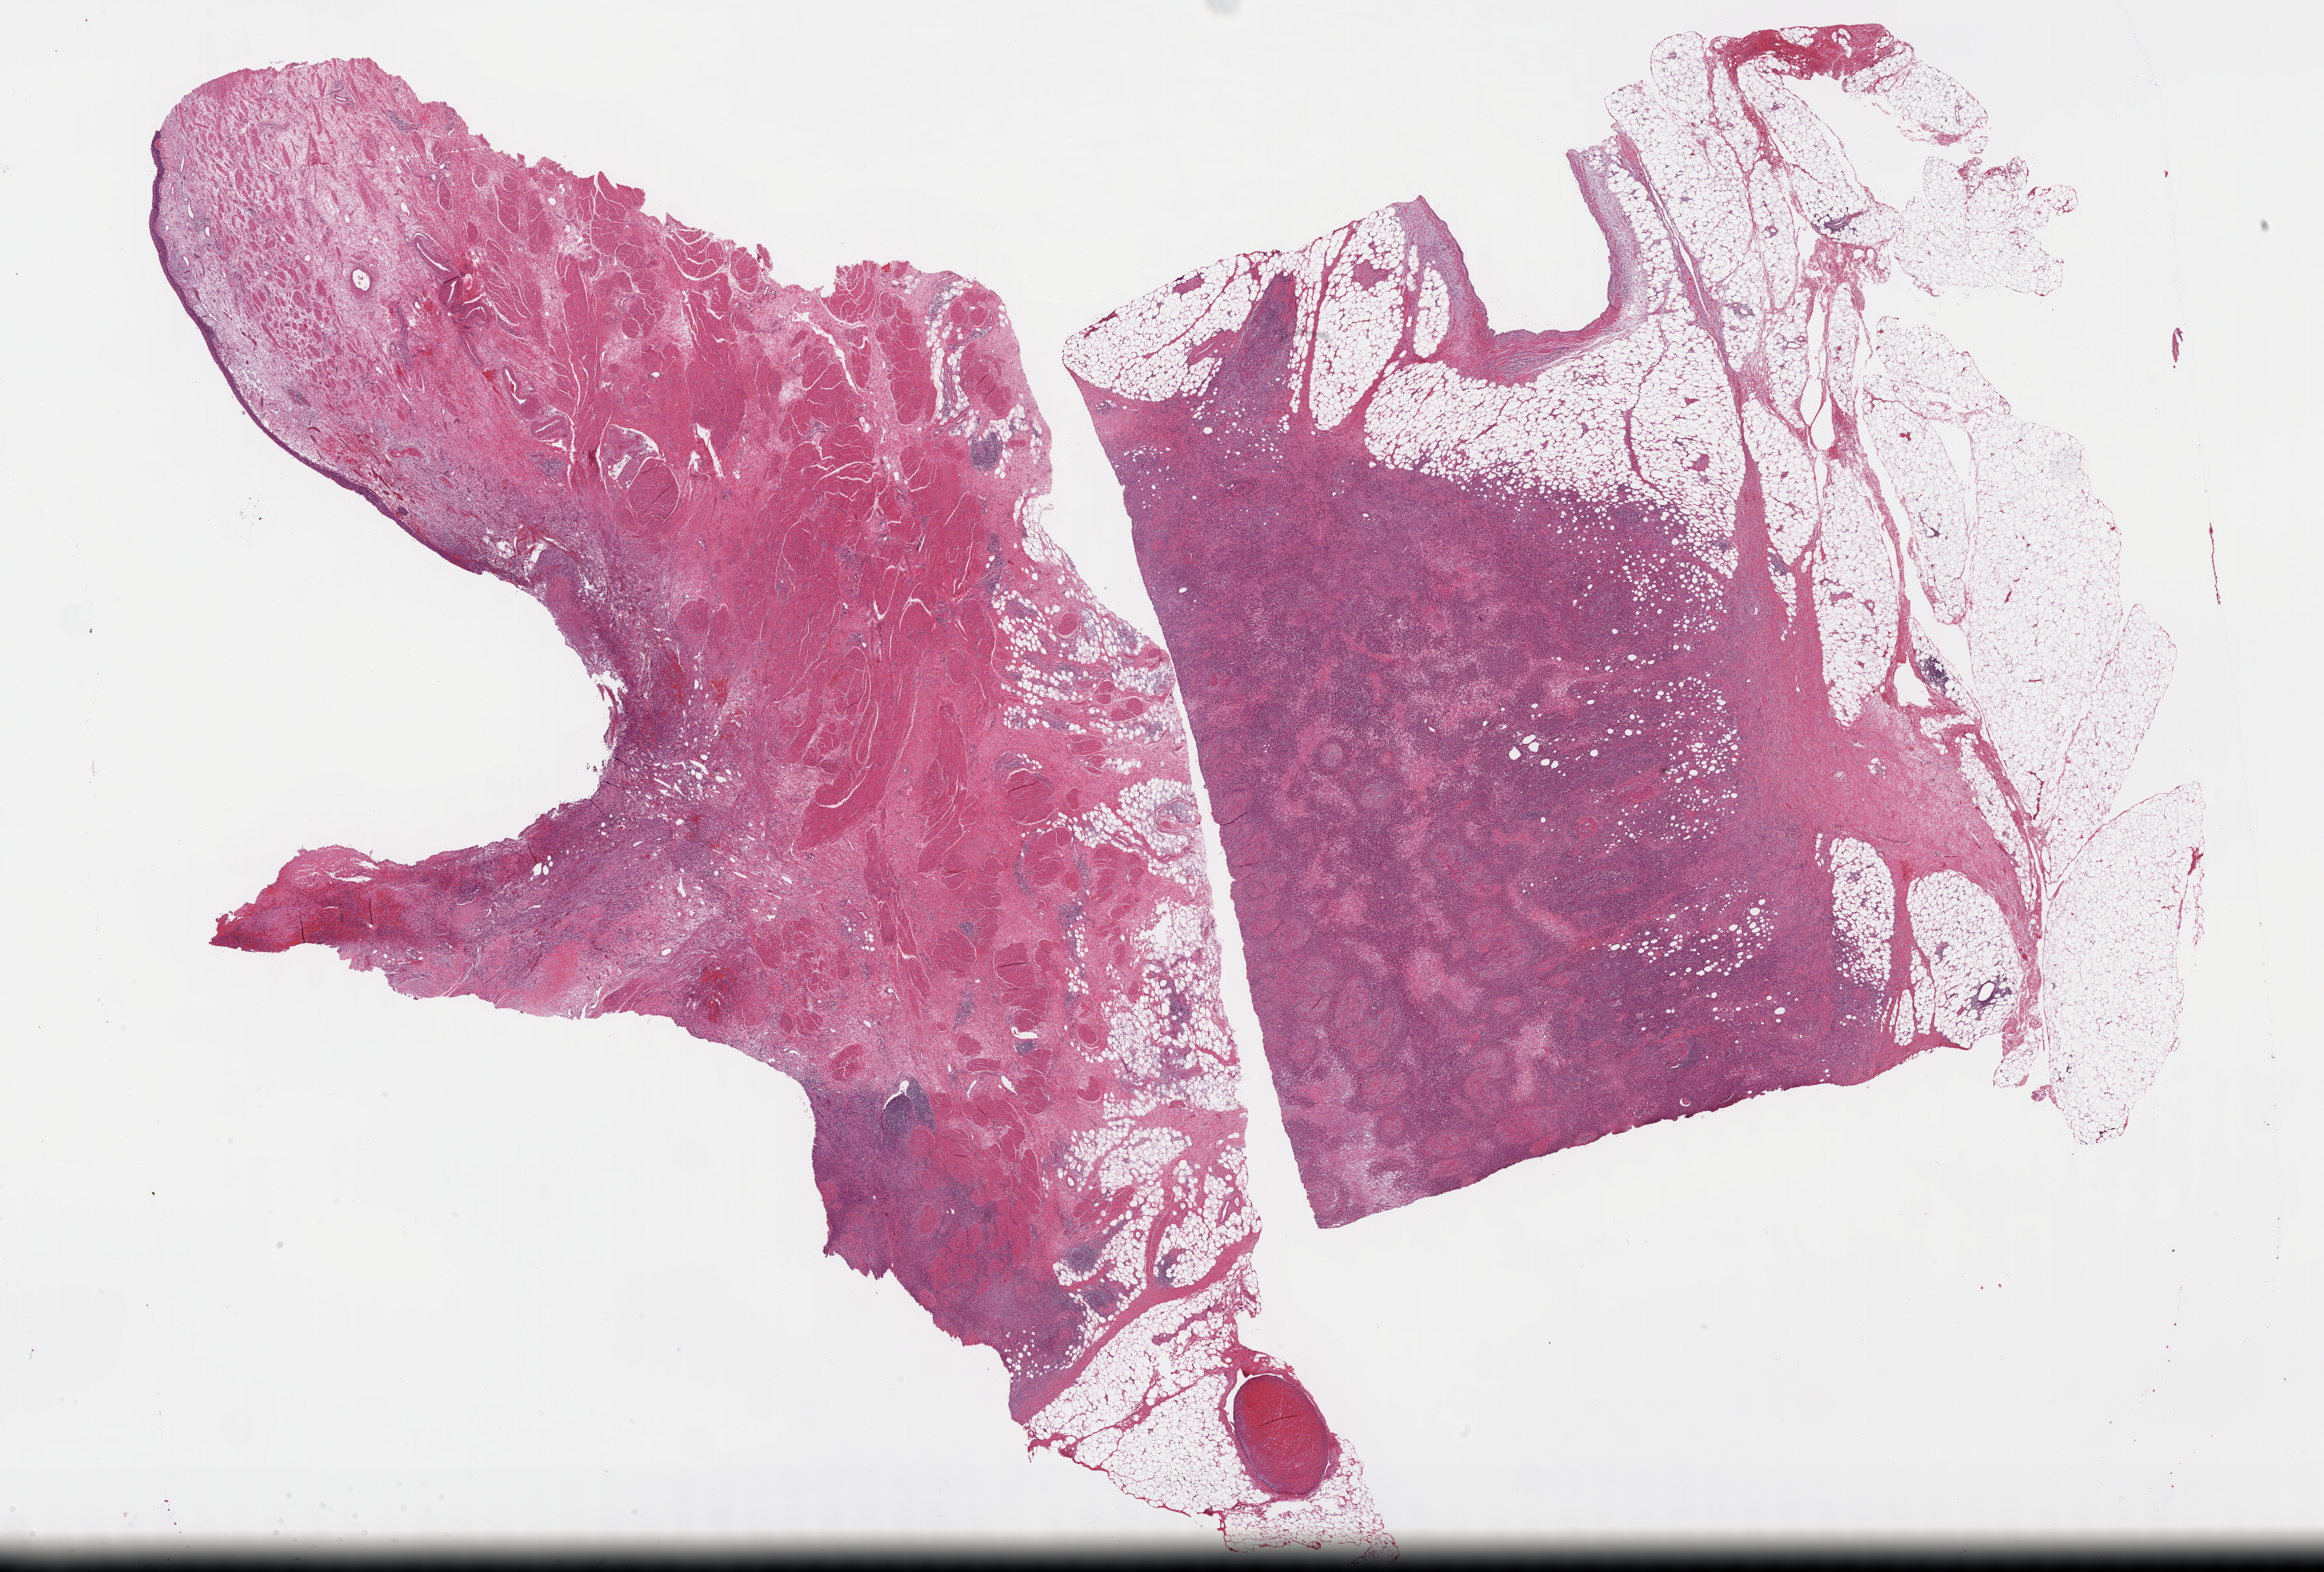
H&E-stained whole-slide image — shown as a low-resolution overview of the whole scanned area (about 31.7 x 21.4 mm, acquisition: 40x scan), formalin-fixed paraffin-embedded (FFPE) diagnostic section, bladder, primary tumour sample. Male, age 69 years at initial diagnosis. Histologic grade: high grade.
* AJCC pathologic stage: III (7th edition)
* diagnosis: Transitional cell carcinoma